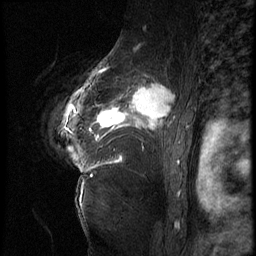
Breast MRI (dynamic contrast-enhanced), one sagittal slice; position 50 of 62 along the scan axis; 3 images stored at this slice position (order not interpretable as contrast timing); 1.5 T; TE 4.2 ms, TR 9 ms; 256 × 256 image matrix. Female patient, age 56 years. From the clinical record (not read from this slice): setting: breast cancer imaged before/during neoadjuvant chemotherapy; receptor status: HER2-positive.
Outlined on this slice (semi-automatic segmentation, software-assisted and operator-edited):
- analysis volume of interest (the breast-tissue region the enhancement analysis was run in; not a lesion): bounding box [x1, y1, x2, y2] px = [84, 75, 181, 153]
- tumour enhancement mask (voxels above the 140 % enhancement threshold inside the analysis volume of interest): [89, 75, 175, 139]